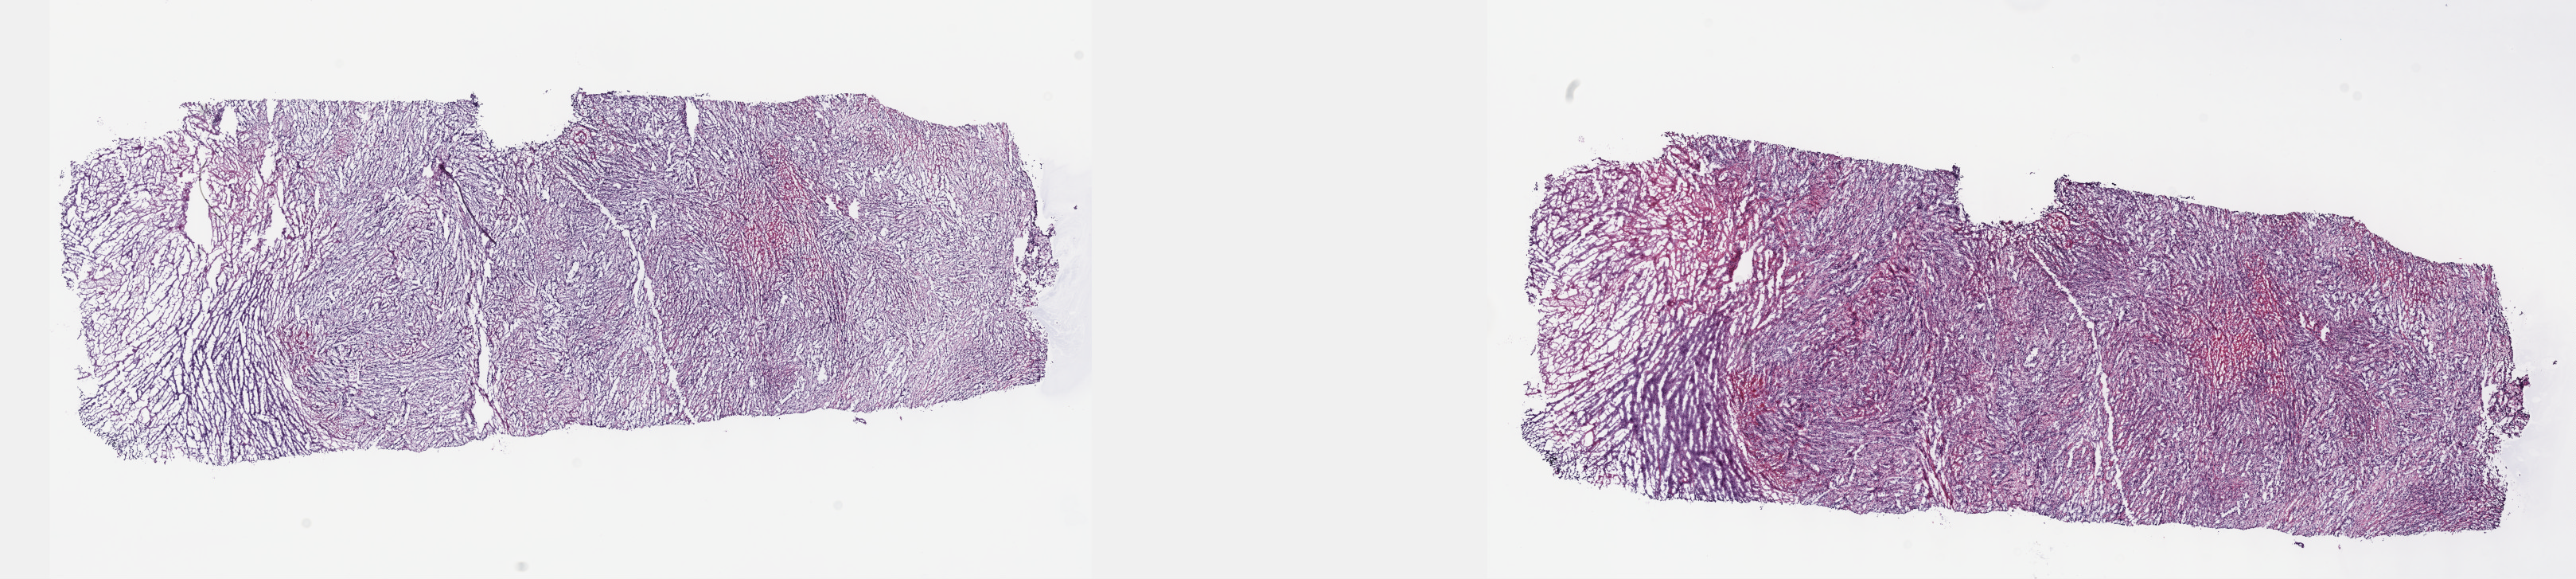
H&E whole-slide image — a low-resolution overview of the entire scanned area, about 26.2 x 5.9 mm. Frozen section from the top of the tissue portion. Bladder, primary tumour sample. Female patient; age at initial diagnosis 60 years. Histologic grade: high grade. Composition of this section per pathologist review: tumour cells 70%, tumour nuclei 70%, normal cells 0%, stromal cells 15%, necrosis 15%. Inflammatory infiltration, as recorded: lymphocyte infiltration 2%, monocyte infiltration 1%, neutrophil infiltration 4%.
- TNM: T3b N2 MX
- histologic diagnosis: Transitional cell carcinoma
- AJCC pathologic stage: IV (6th edition)
- lymph nodes positive (case pathology): 2 of 86 examined